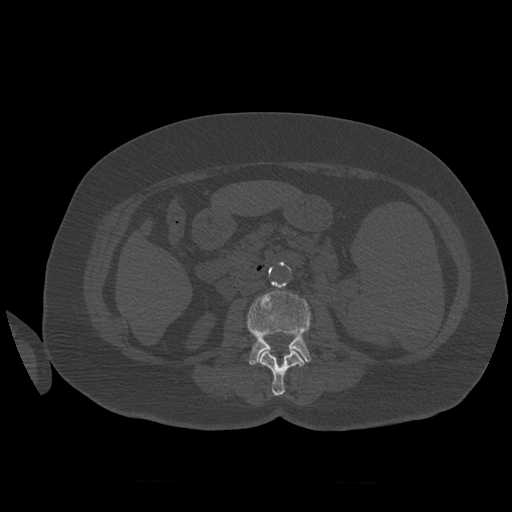
CT including the spine, one axial slice; slice 240 of 399 in the series (ordered by position); reconstruction kernel STANDARD; bone window (W 1800 / L 400 HU); 512 × 512 image matrix, field of view 404 × 404 mm. Patient age 81 years. Case-level facts recorded for this patient, not image findings: primary cancer: renal; vertebrae with lytic lesions (as recorded): L1.
Outlined on this slice (semi-automatically segmented with operator editing):
- L2 vertebra: bounding box (x1, y1, x2, y2) in pixels: (259, 347, 305, 396)
- L3 vertebra: (247, 289, 311, 365)